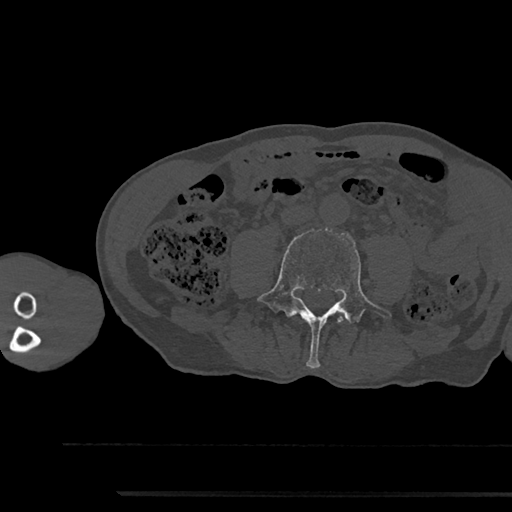
CT including the spine, one axial slice; slice 422 of 797 in the series (ordered by position); 120 kVp; bone window (W 1800 / L 400 HU); 0.5 mm slice thickness; 512 × 512 image matrix, field of view 367 × 367 mm. Male patient, age 79 years. From the clinical record (not read from this slice): primary cancer: prostate.
Annotated regions visible in this slice (semi-automatic segmentation, software-assisted and operator-edited):
- L4 vertebra: box from (x=254, y=227) to (x=392, y=368) px